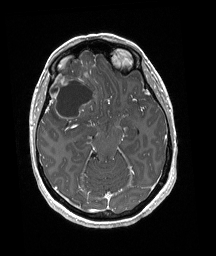
Brain MRI from a brain-tumour surgery series, one axial slice. Slice 116 of 192 in the series (ordered by position). T1-weighted post-contrast. 1 mm slice thickness. 216 × 256 image matrix, field of view 211 × 250 mm. From the clinical record (not read from this slice): histopathology: Oligodendroglioma; WHO grade: 3; IDH mutation: yes; tumour location: Right Frontal.
Annotated regions visible in this slice (manually delineated by an expert):
- tumour: box from (x=48, y=60) to (x=97, y=124) px